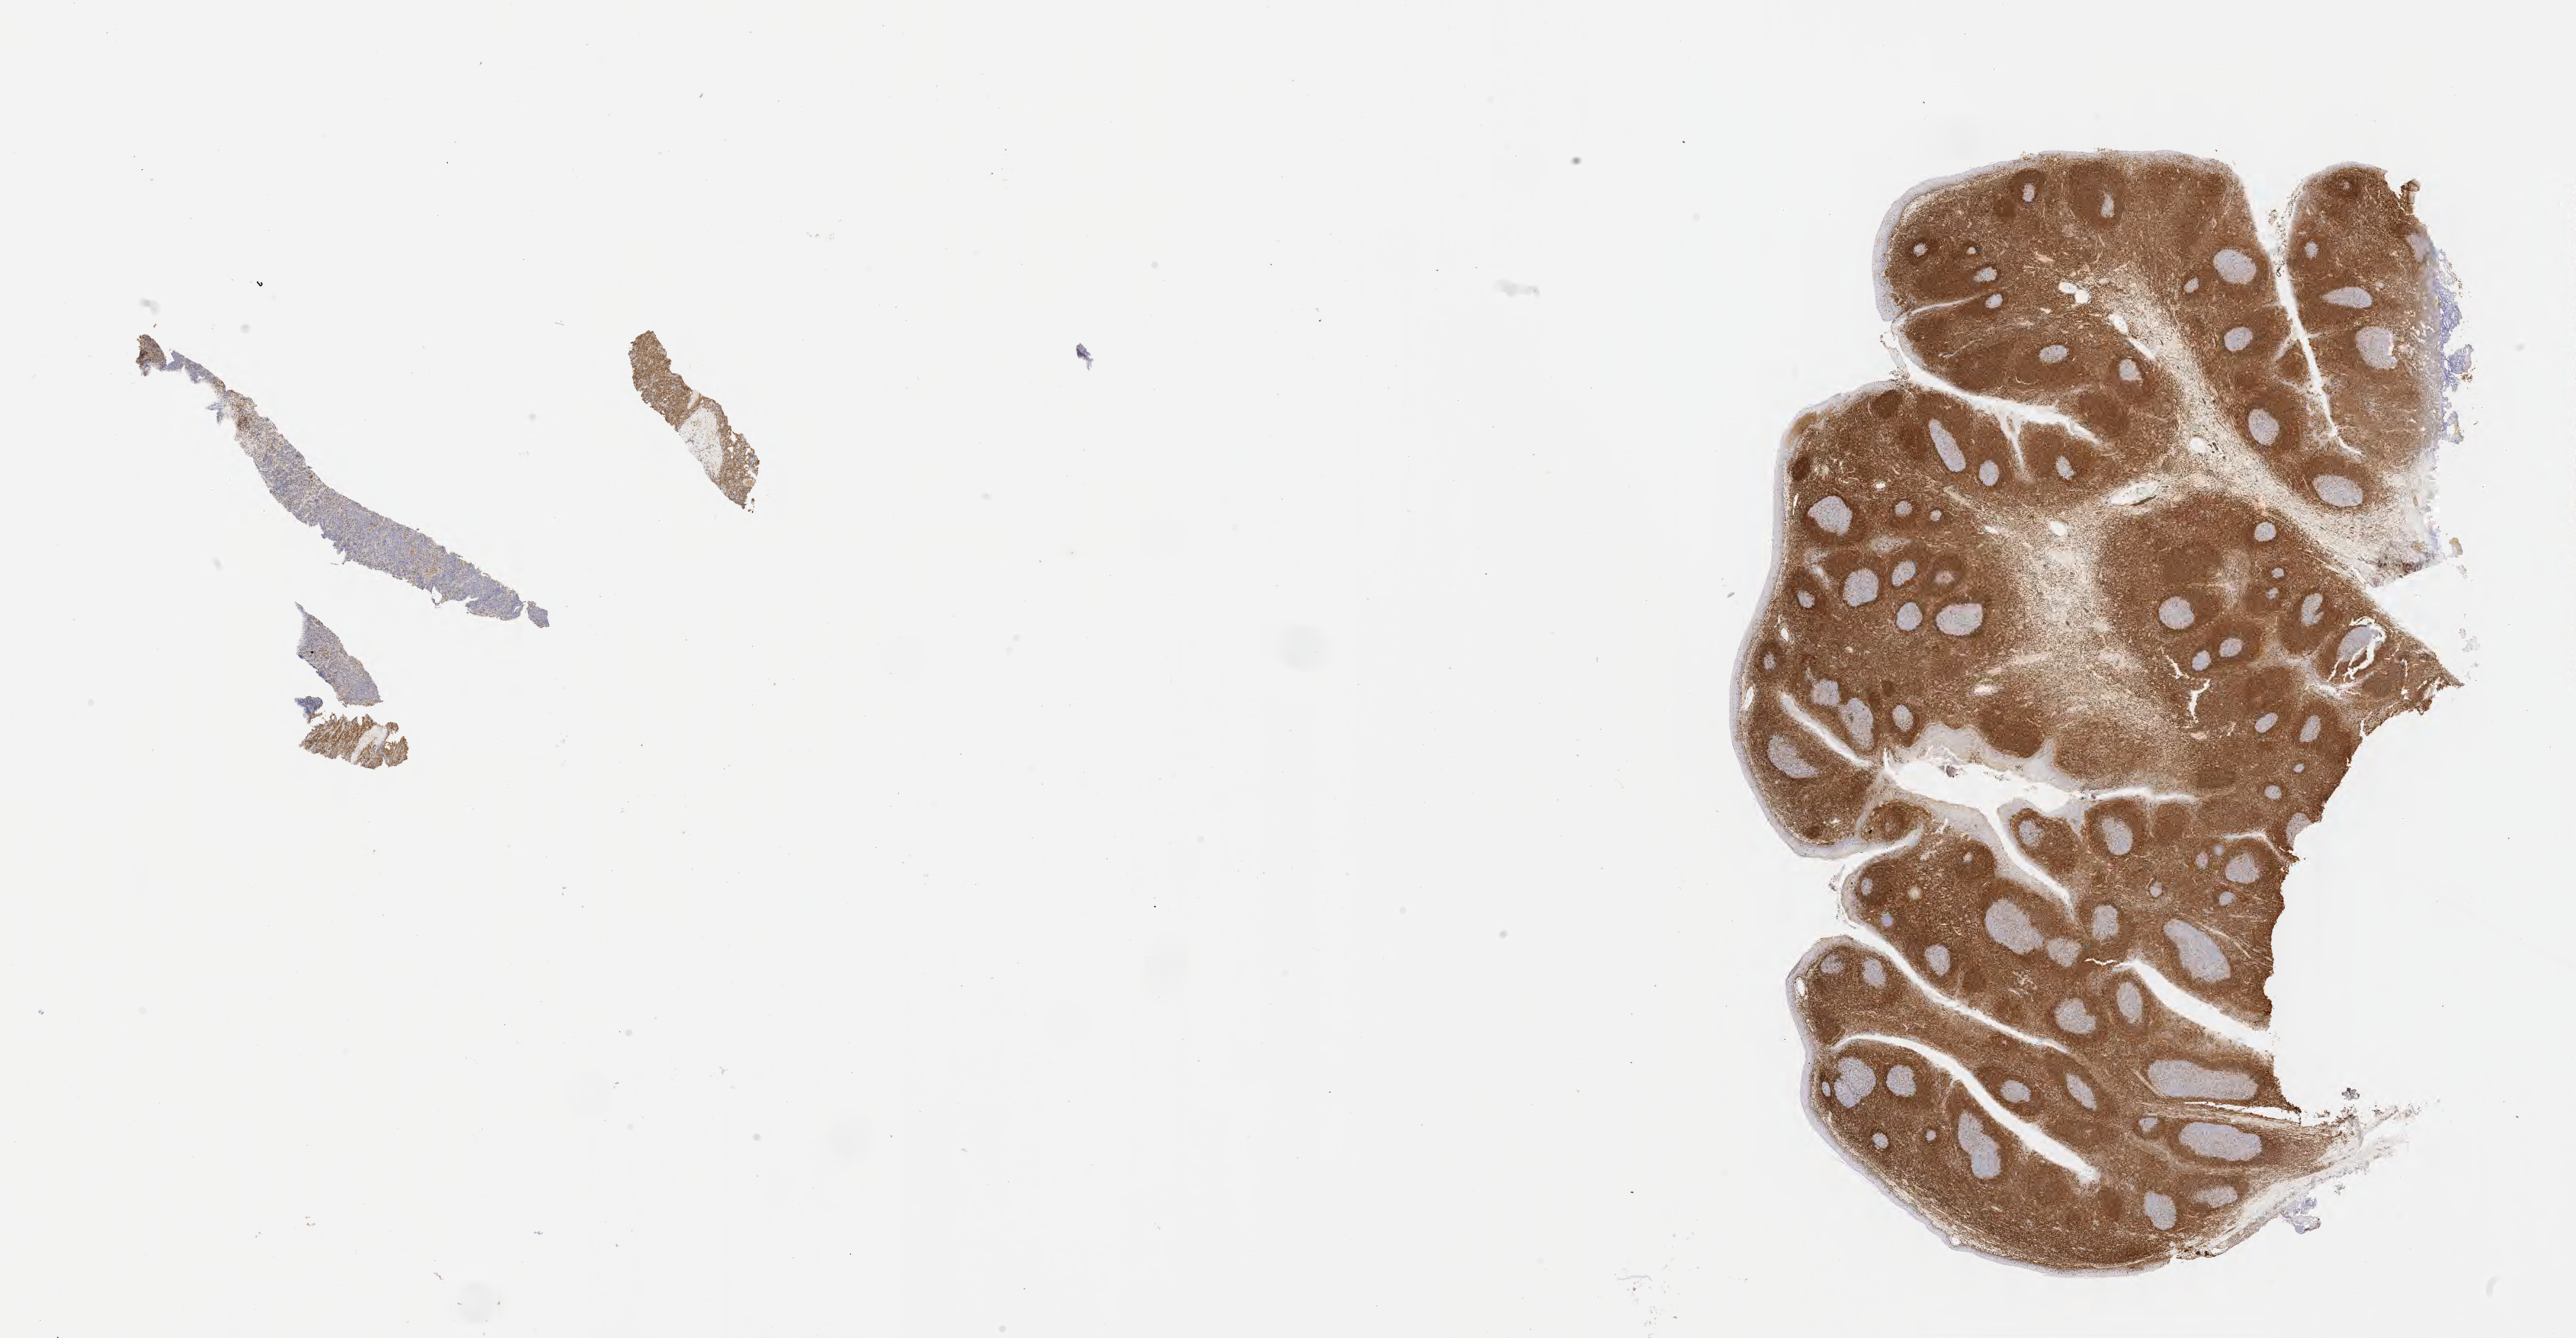
Immunohistochemistry (IHC) whole-slide image stained for BCL2, whole scanned area (about 28.7 x 14.9 mm) shown as a low-resolution overview. Tumor tissue. Patient male; aged 13.
Diagnosis: Diffuse large B-cell lymphoma, NOS.